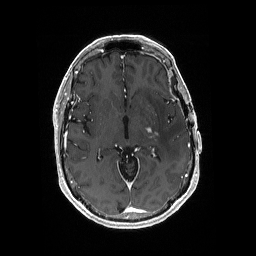
Brain MRI from a brain-tumour surgery series, one axial slice; slice 104 of 176 in the series (ordered by position); T1-weighted post-contrast; 1 mm slice thickness; 256 × 256 image matrix, field of view 256 × 256 mm. From the clinical record (not read from this slice): histopathology: Glioblastoma; WHO grade: 4; IDH mutation: no; tumour location: Left Medial Temporal.
Outlined on this slice (manually delineated by an expert):
- tumour: box from (x=146, y=127) to (x=158, y=139) px